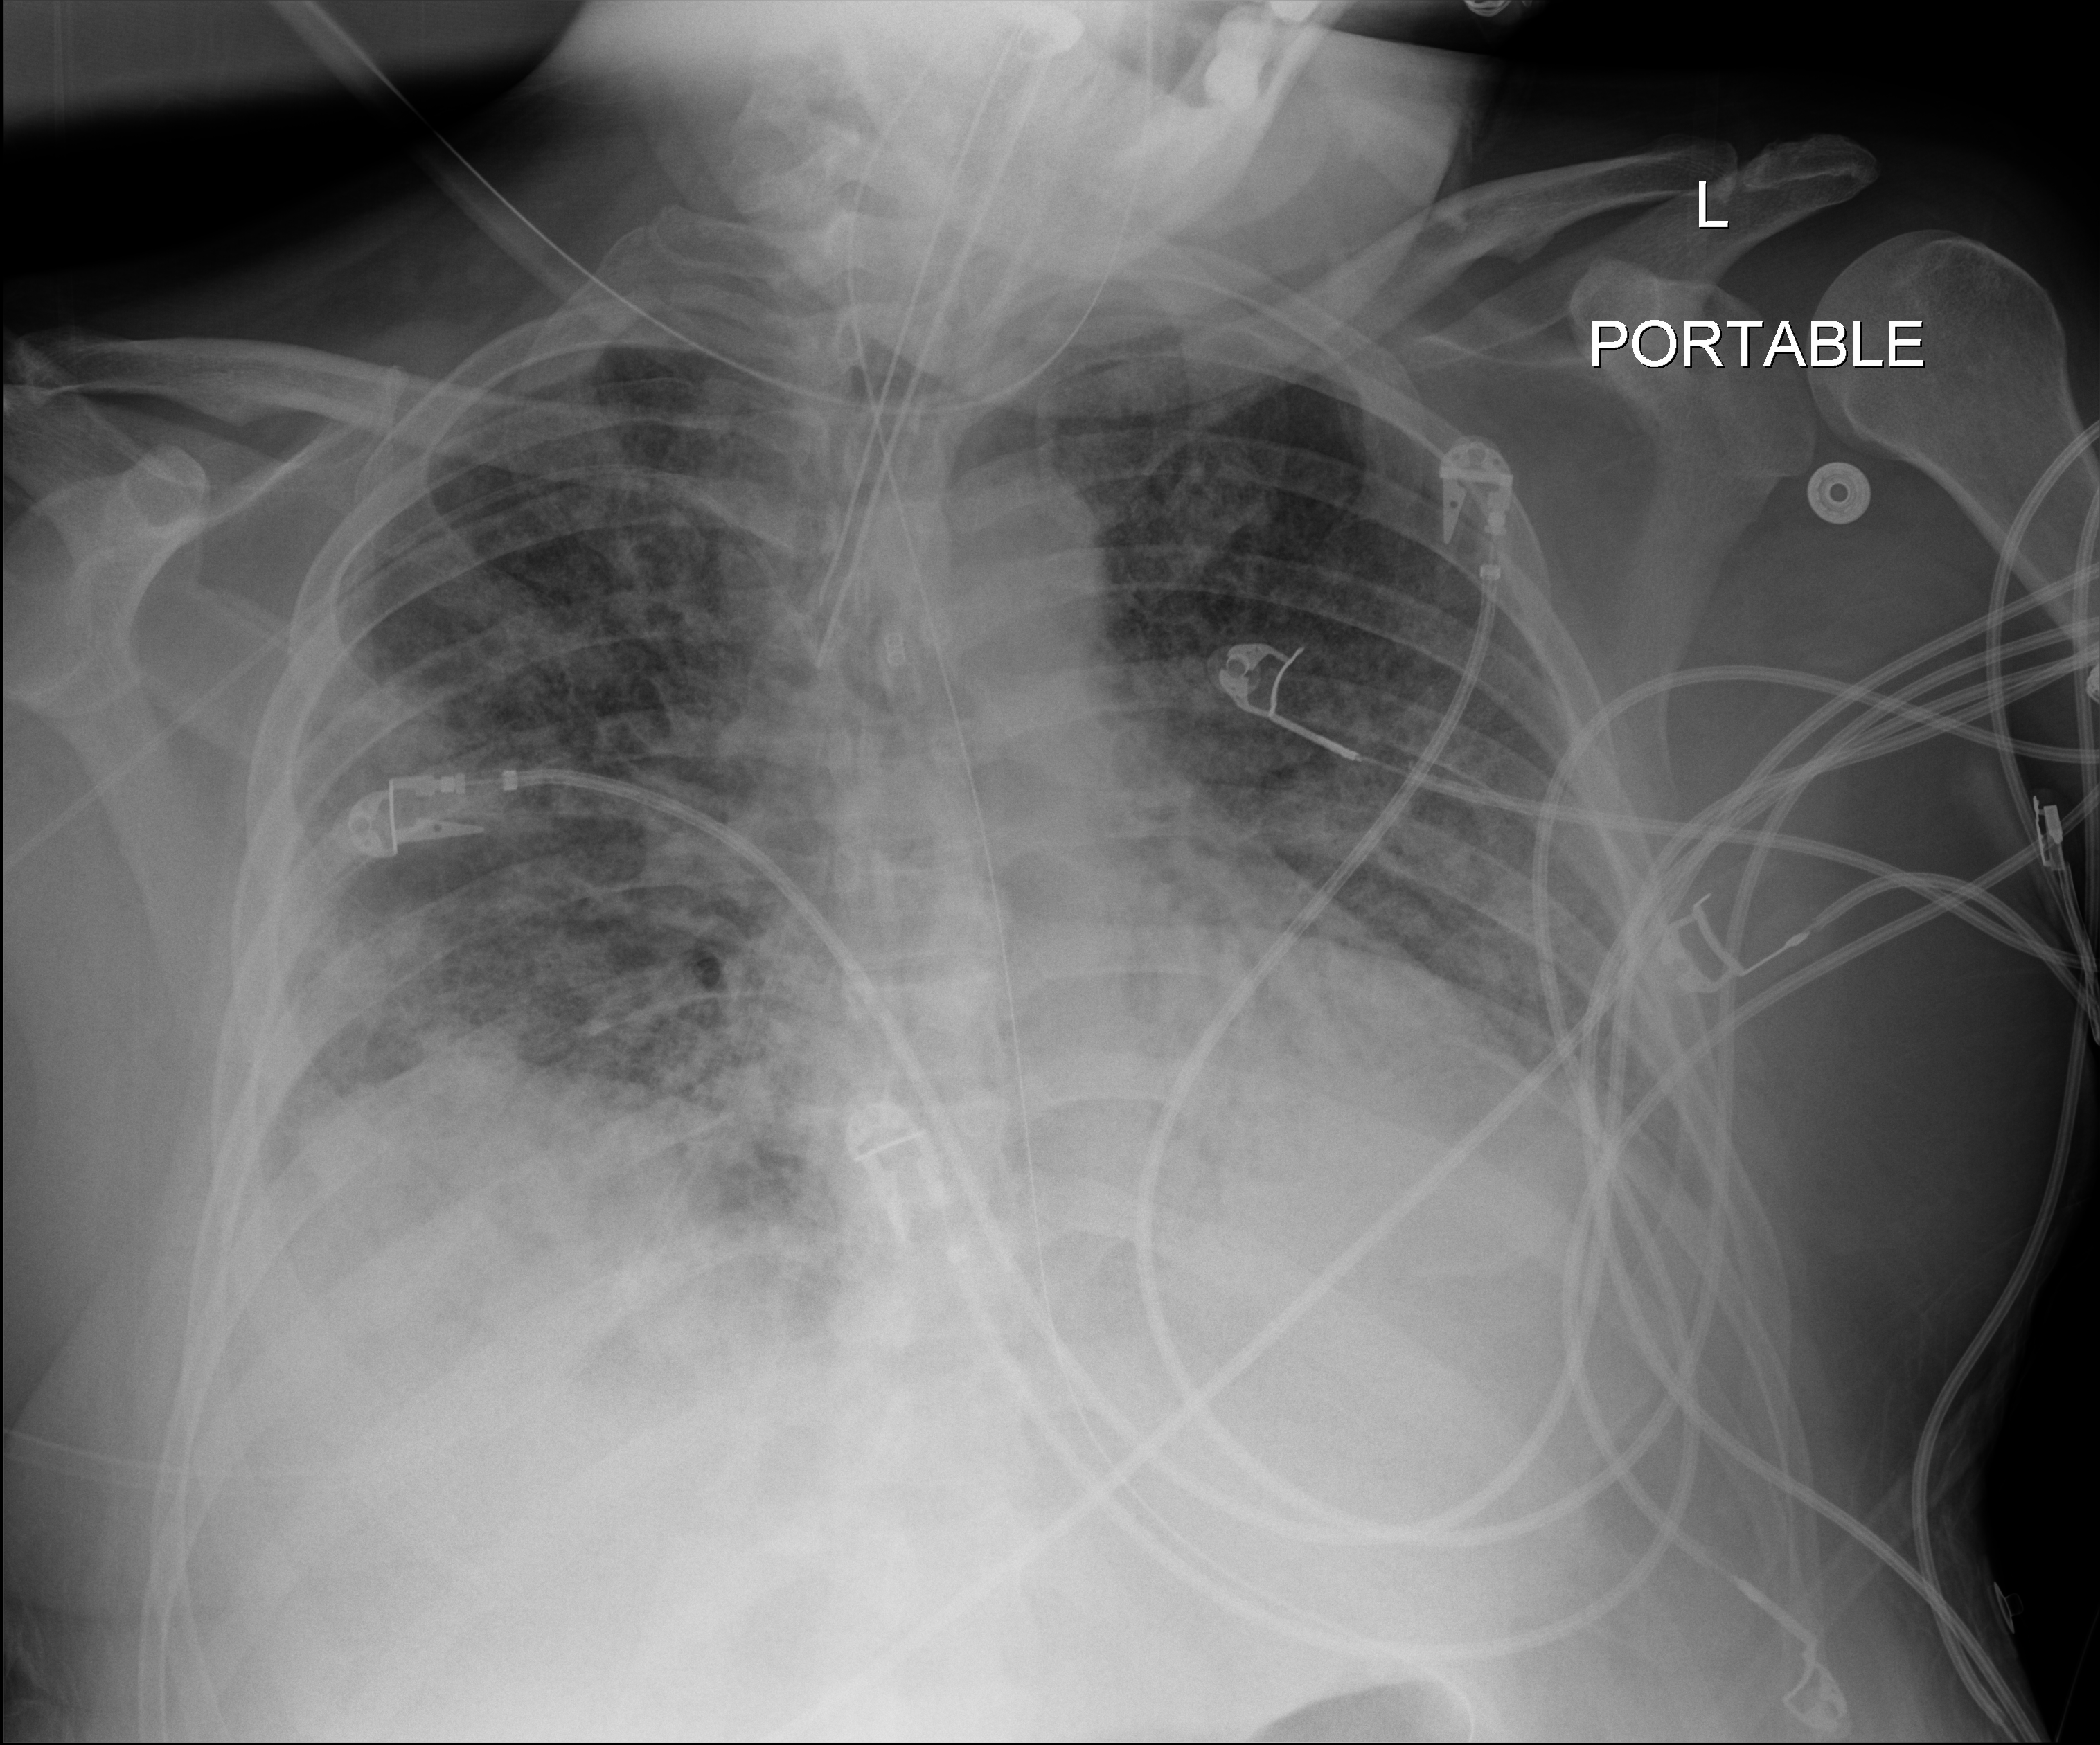
Portable chest radiograph, anteroposterior (AP) projection. Male patient hospitalised with COVID-19, age 18–59 years.
Hospital-stay facts (about this admission, not read from this image; timing relative to this image not recorded): admitted to intensive care during this hospital stay: yes.